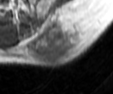
MRI of an extremity soft-tissue mass, one axial slice; slice 30 of 42 in the series (ordered by position); MR volume resampled by the dataset authors to the PET/CT grid (not the native acquisition matrix); 3.27 mm slice thickness; 113 × 94 image matrix. Male patient. Case-level facts recorded for this patient, not image findings: histological type: leiomyosarcoma; grade: intermediate; site of the primary tumour: left pelvis.
Outlined on this slice (expert contour drawn on MRI and transferred to this co-registered scan by the dataset authors):
- gross tumour volume (mass): bounding box <28,18,86,67> (left, top, right, bottom; pixels)